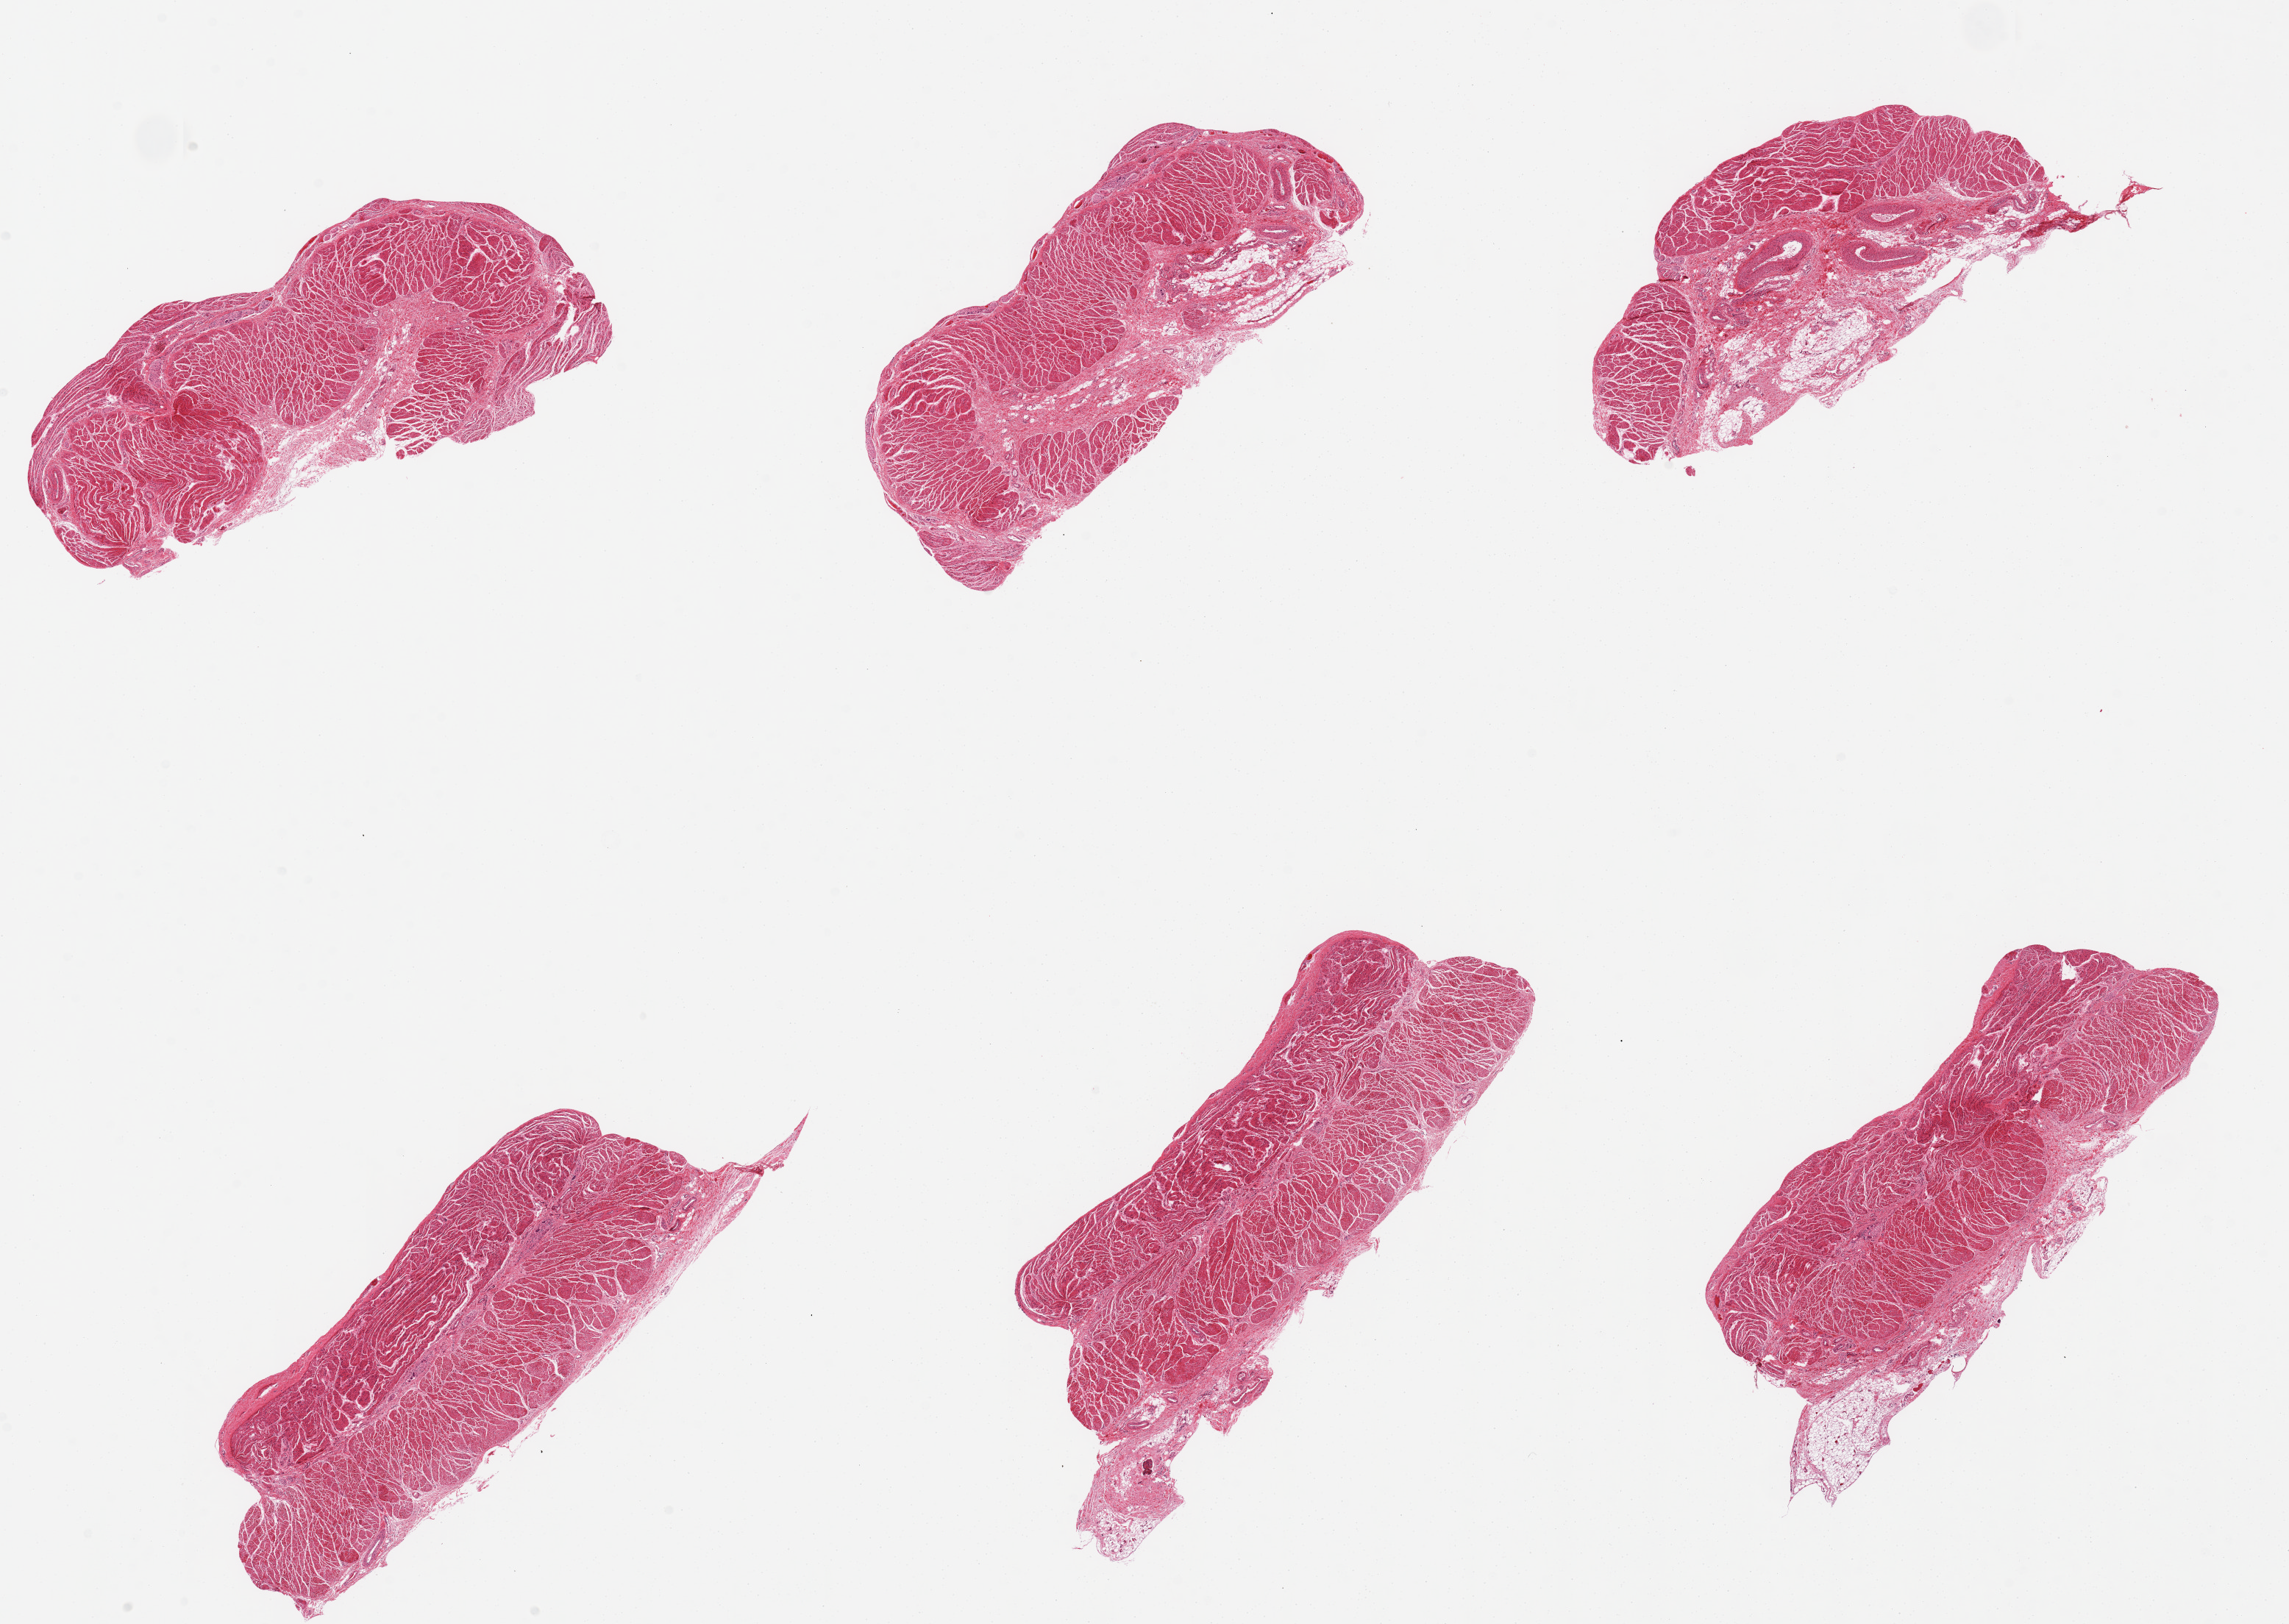
Digitized hematoxylin and eosin (H&E)-stained section — a low-resolution overview of the entire scanned area, about 24.6 x 17.5 mm (slide scanned at 20x), PAXgene-fixed paraffin-embedded (PFPE) section, target tissue: gastroesophageal junction, tissue donor sample.
Reviewer comment on this tissue sample: 6 pieces, all muscularis, few nubbins adherent fat up to ~1mm.